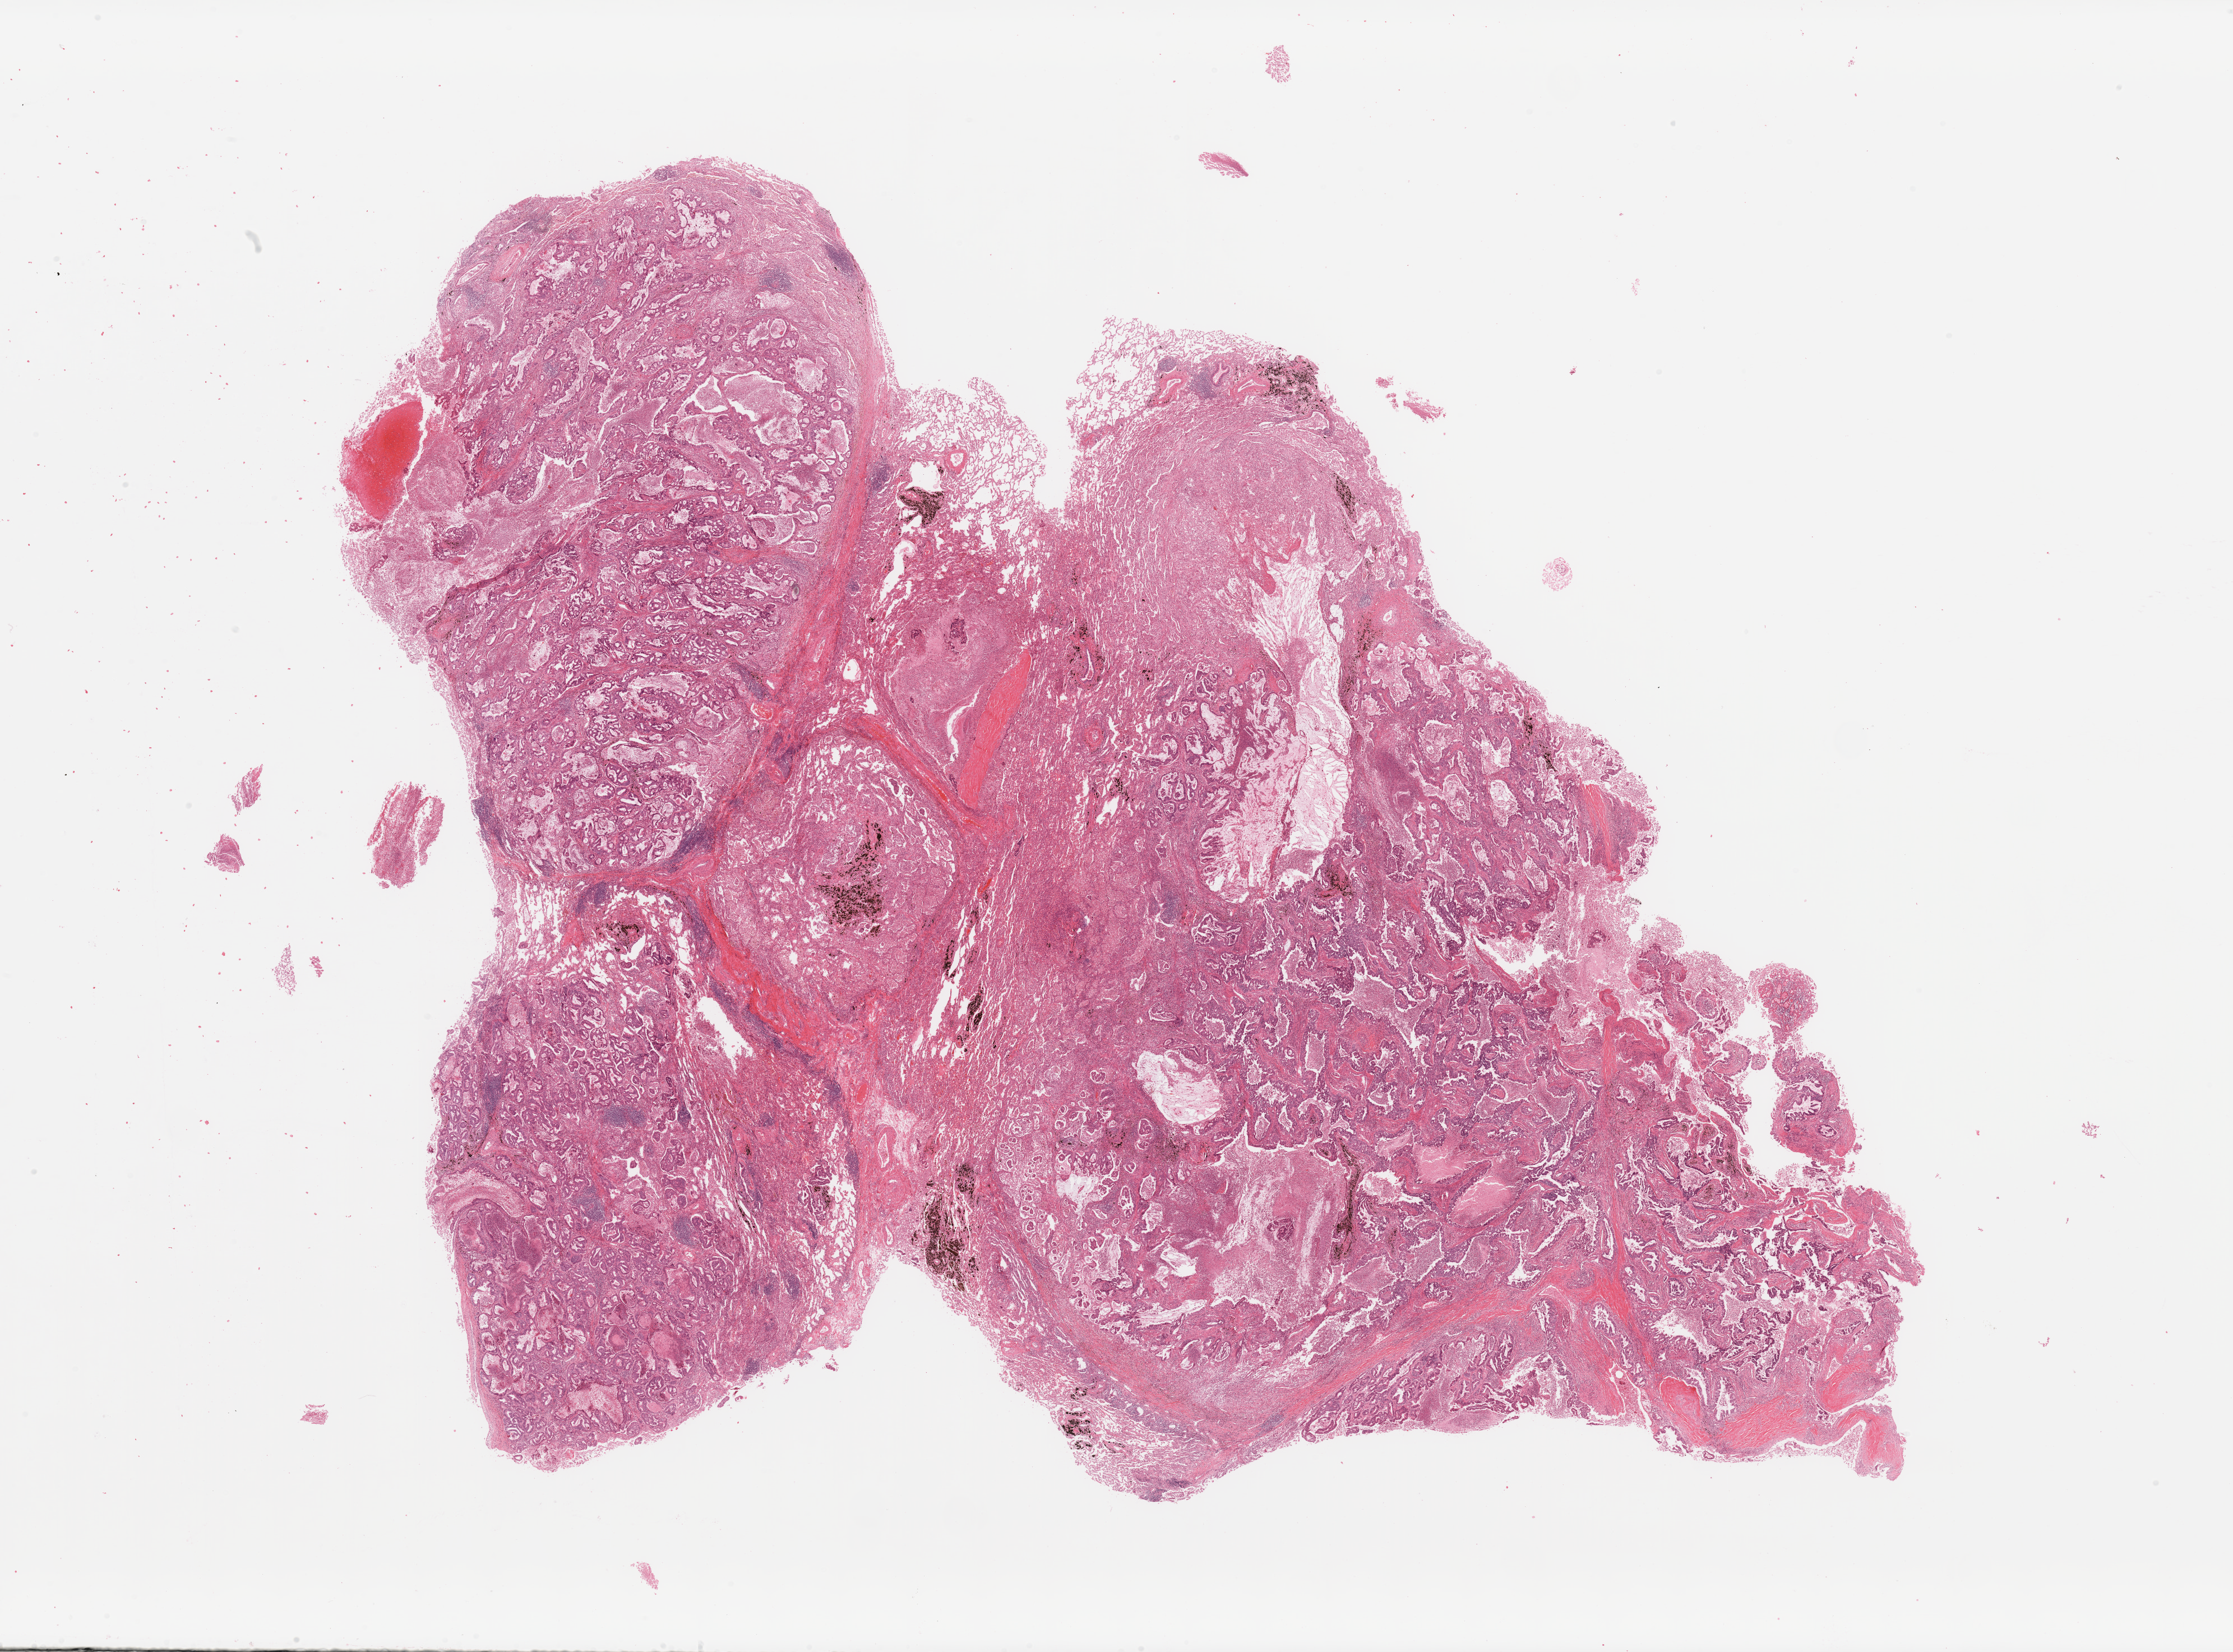
Hematoxylin and eosin (H&E) stained whole-slide image — low-resolution overview of the scanned area, about 31.5 x 23.3 mm; tumour tissue sample, sampled site: lung. Patient: male, age 49 years. Histologic grade: G2 (moderately differentiated). Composition of this section per pathologist review: tumour nuclei 70%, necrosis 10%.
• histologic diagnosis: Adenocarcinoma, NOS
• AJCC pathologic stage: IIB